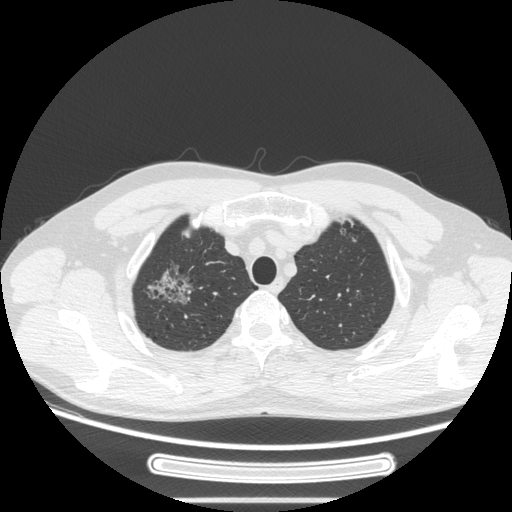
Chest CT, one axial slice; slice 224 of 269 in the series (ordered by position); reconstruction kernel STANDARD; lung window (W 1500 / L -600 HU); 1.25 mm slice thickness; 512 × 512 image matrix, field of view 382 × 382 mm. Male patient, age 53 years. From the clinical record (not read from this slice): clinical TNM (as recorded): T1c N0 M0; histopathological grade: G2.
Outlined on this slice (bounding box drawn by a radiologist):
- lung tumour (recorded histology: adenocarcinoma): bounding box (x1, y1, x2, y2) in pixels: (139, 259, 197, 312)